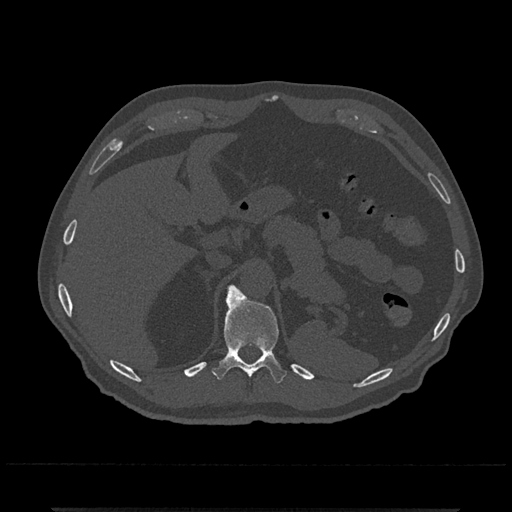
CT including the spine, one axial slice; position 493 of 797 along the scan axis; reconstruction kernel Br40s/3; 120 kVp; bone window (W 1800 / L 400 HU); 512 × 512 image matrix, field of view 393 × 393 mm. Male patient, age 67 years. Case-level facts recorded for this patient, not image findings: primary cancer: prostate.
Annotated regions visible in this slice (semi-automatically segmented with operator editing):
- T11 vertebra: bounding box (x1, y1, x2, y2) in pixels: (212, 284, 287, 384)